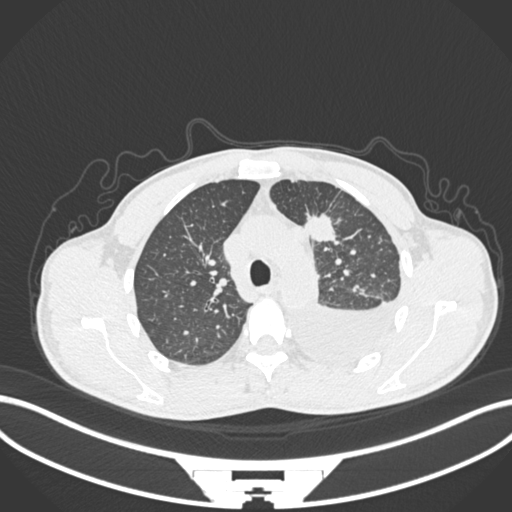
Chest CT, one axial slice. Slice 158 of 244 in the series (ordered by position). 120 kVp. Lung window (W 1500 / L -600 HU). 1 mm slice thickness. 512 × 512 image matrix, field of view 400 × 400 mm. Patient: male, 49 years. From the clinical record (not read from this slice): clinical TNM (as recorded): T1c N1 M1.
Outlined on this slice (bounding box drawn by a radiologist):
- lung tumour (recorded histology: adenocarcinoma): bounding box <304,204,338,246> (left, top, right, bottom; pixels)